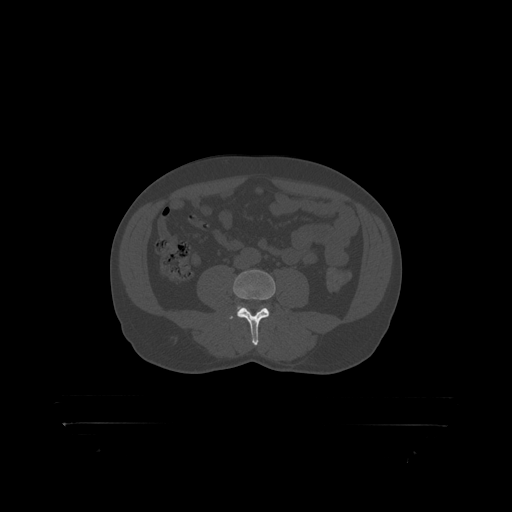
CT including the spine, one axial slice. Position 229 of 399 along the scan axis. Reconstruction kernel STANDARD. Bone window (W 1800 / L 400 HU). 1.25 mm slice thickness. 512 × 512 image matrix, field of view 650 × 650 mm. Male patient, age 46 years. From the clinical record (not read from this slice): primary cancer: skin.
Structures marked on this image (semi-automatically segmented with operator editing):
- L4 vertebra: bounding box (x1, y1, x2, y2) in pixels: (233, 270, 276, 319)
- L5 vertebra: (238, 307, 240, 309)